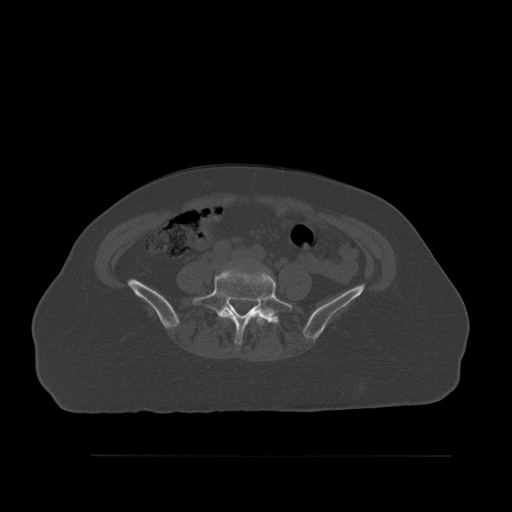
CT including the spine, one axial slice; position 192 of 527 along the scan axis; bone window (W 1800 / L 400 HU); 1.5 mm slice thickness; 512 × 512 image matrix, field of view 470 × 470 mm. Patient: female, 73 years. Case-level facts recorded for this patient, not image findings: primary cancer: breast; vertebrae with lytic lesions (as recorded): L2.
Annotated regions visible in this slice (semi-automatically segmented with operator editing):
- L4 vertebra: box from (x=223, y=309) to (x=264, y=326) px
- L5 vertebra: (x=193, y=269)–(x=292, y=345)